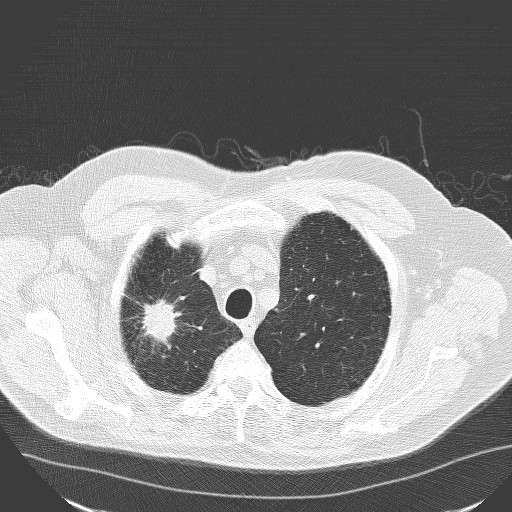
Low-dose screening chest CT, axial slice; baseline screening round; lung window (W 1500 / L -600 HU); 3.2 mm slice thickness; lung (sharp) reconstruction kernel (D); slice 136 of 160 in the series. Male, age 71 years at enrolment.
Lesion marked by an expert reader, box from (x=116, y=282) to (x=189, y=357) px. Reader record for this screening exam (exam-level; its link to the box is not recorded): non-calcified nodule or mass ≥4 mm, right upper lobe, 30 × 25 mm, spiculated (stellate) margins, soft tissue attenuation. Participant outcome: lung cancer diagnosed 182 days after this screen — squamous cell carcinoma, NOS, right upper lobe, poorly differentiated (G3), stage IA (AJCC 6th edition), 30 mm at pathology.